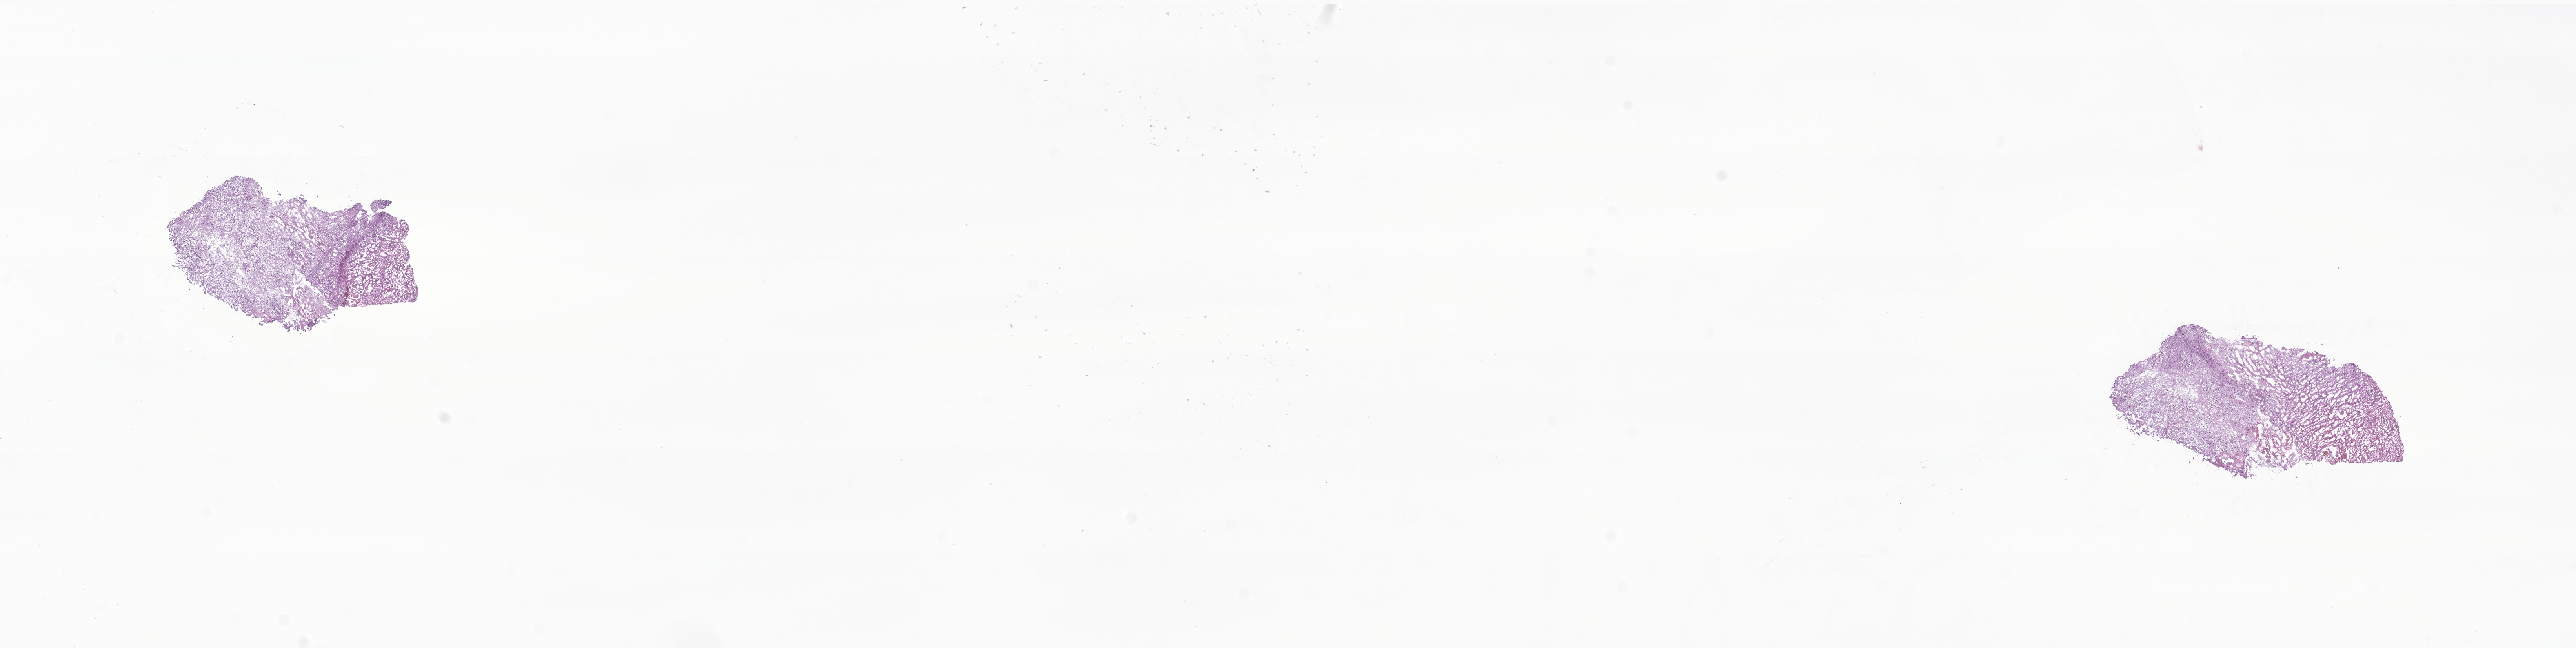
Whole-slide image, H&E stain of tumor tissue from the brain, a low-resolution overview of the entire scanned area, about 27.7 x 7.0 mm, cryosection (OCT / tissue freezing medium). Patient male; age 131 months (10 years 11 months).
• recorded diagnosis: Pilocytic astrocytoma